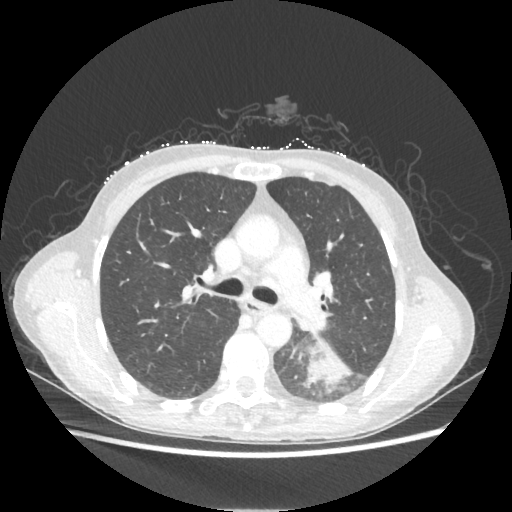
Chest CT, one axial slice. Reconstruction kernel STANDARD. 80 kVp. Lung window (W 1500 / L -600 HU). 1.25 mm slice thickness. 512 × 512 image matrix. Patient: female, 53 years. Case-level facts recorded for this patient, not image findings: clinical TNM (as recorded): T3 N0 M0.
Annotated regions visible in this slice (bounding box drawn by a radiologist):
- lung tumour (recorded histology: adenocarcinoma): bounding box (x1, y1, x2, y2) in pixels: (308, 339, 351, 387)